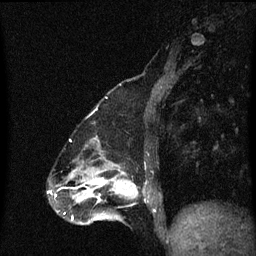
Breast MRI (dynamic contrast-enhanced), one sagittal slice. Slice 22 of 60 in the series (ordered by position). Dynamic contrast-enhanced series, image 2 of 3 at this slice position (ordered by acquisition). 1.5 T. TE 4.2 ms, TR 8.4 ms. 256 × 256 image matrix. Patient: female, 47 years.
Structures marked on this image (semi-automatically segmented with operator editing):
- analysis volume of interest (the breast-tissue region the enhancement analysis was run in; not a lesion): box from (x=100, y=172) to (x=151, y=219) px
- tumour enhancement mask (voxels above the 70 % enhancement threshold inside the analysis volume of interest): (x=100, y=172)–(x=138, y=199)